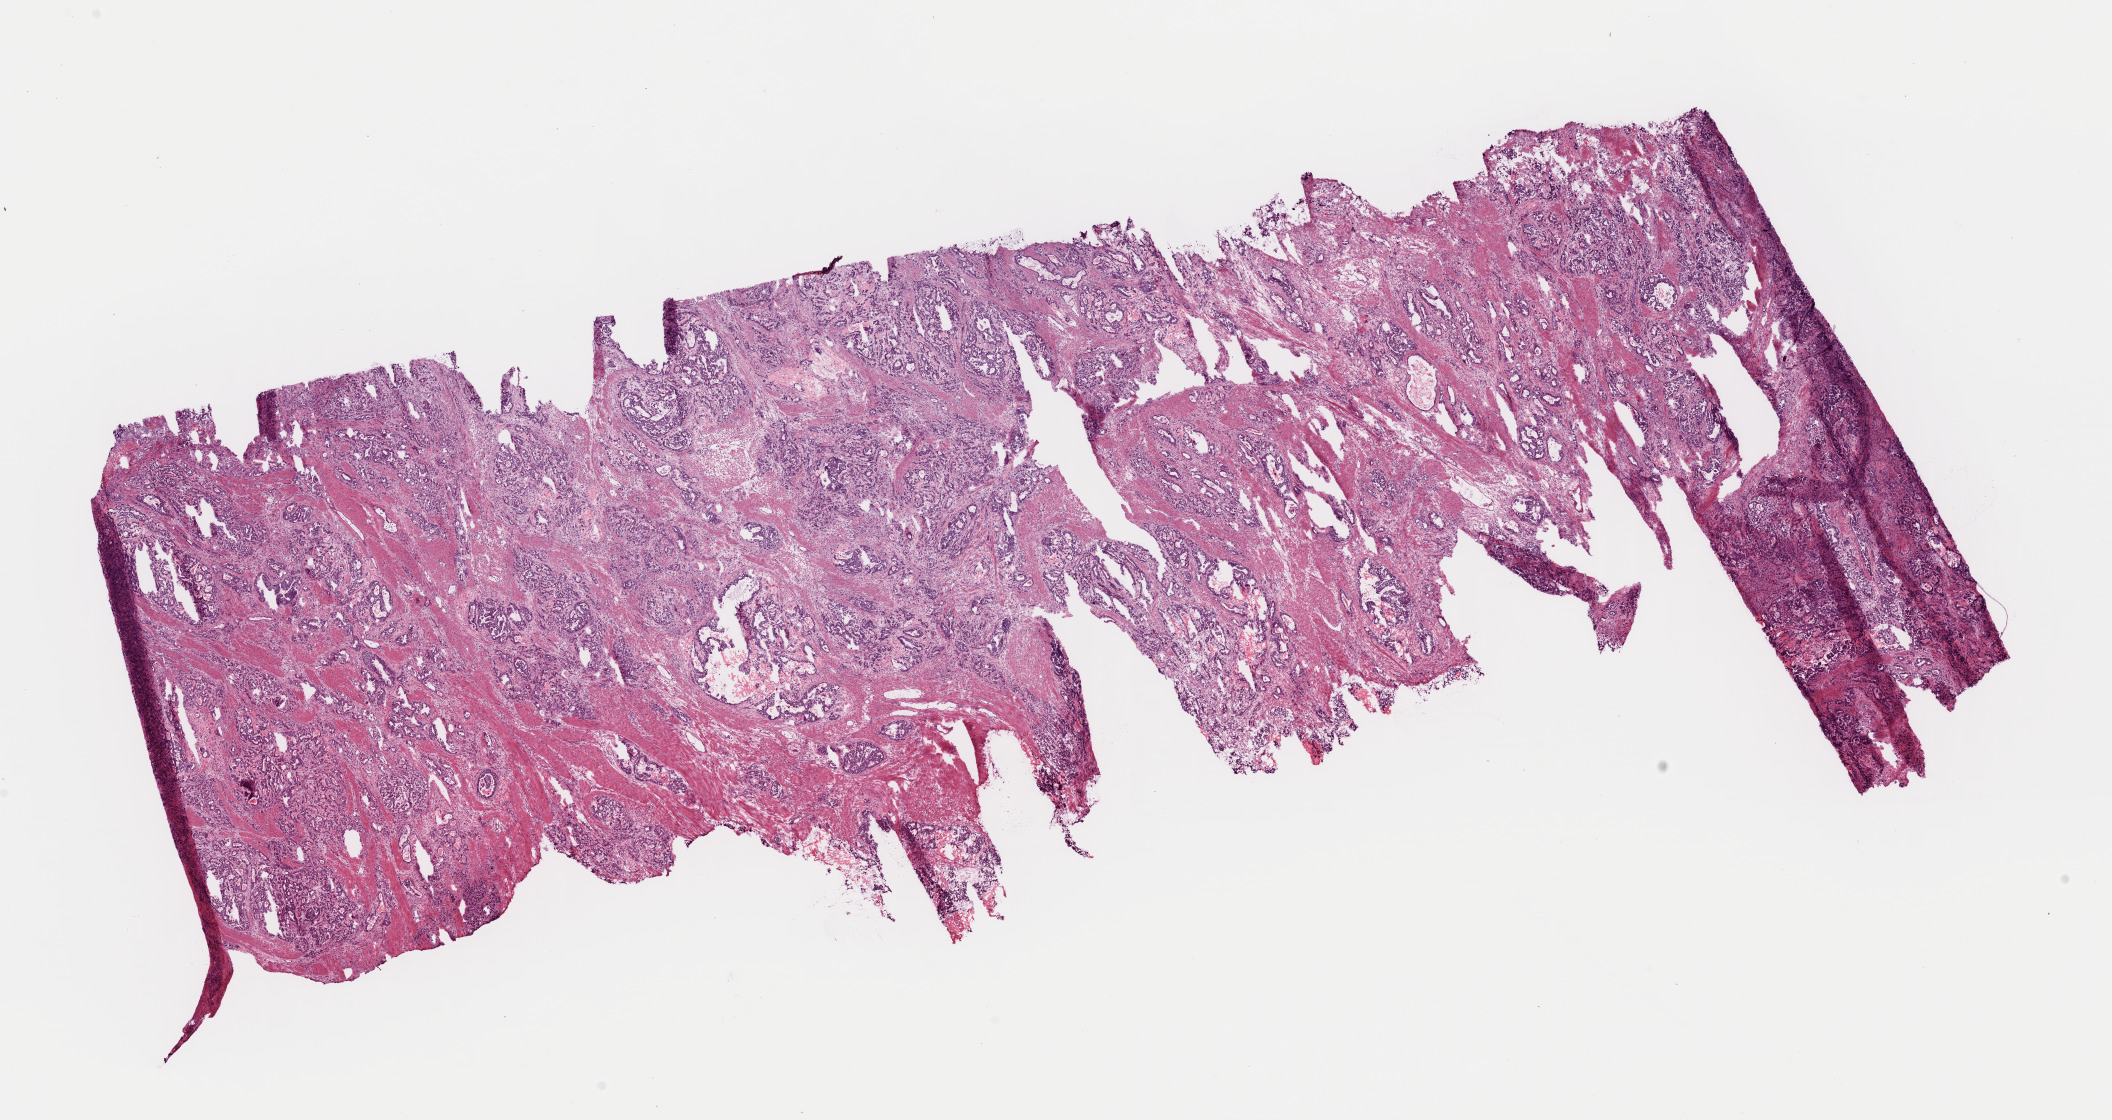
Digitized Hematoxylin and eosin (H&E) stained tissue section (whole slide) — shown as a low-resolution overview of the whole scanned area (about 16.7 x 8.8 mm, slide scanned at 40x), frozen section from the top of the tissue portion, sample: primary tumour, stomach. Female patient; age at initial diagnosis 86 years. Histologic grade: G2 (moderately differentiated). Slide review estimates, as recorded: tumour cells 70%, tumour nuclei 85%, normal cells 0%, stromal cells 20%, necrosis 10%.
* AJCC pathologic stage: IV
* pathologic diagnosis: Adenocarcinoma, NOS (gastric antrum)
* lymph nodes positive (case pathology): 8 of 10 examined